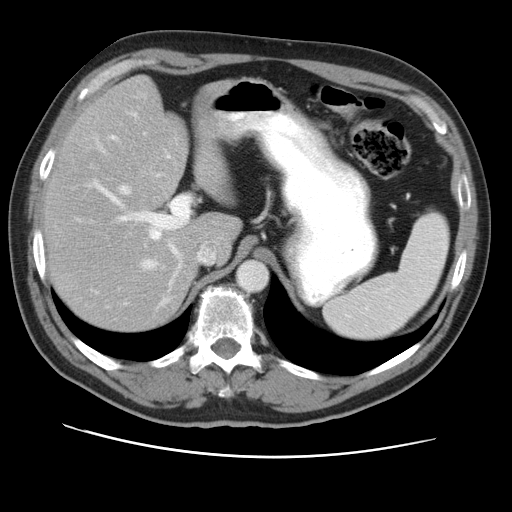
Contrast-enhanced abdominal CT, one axial slice; slice 33 of 49 in the series (ordered by position); reconstruction kernel STANDARD; intravenous contrast given; soft-tissue window (W 400 / L 40 HU); 5 mm slice thickness; 512 × 512 image matrix. Male patient, age 59 years. From the clinical record (not read from this slice): diagnosis: colorectal cancer liver metastases, imaged before liver resection; multiple liver metastases: yes; largest metastasis: 6.3 cm; disease in both lobes: yes.
Annotated regions visible in this slice (expert manual segmentation):
- hepatic veins: bounding box (x1, y1, x2, y2) in pixels: (121, 186, 215, 269)
- liver: (45, 77, 238, 332)
- planned liver remnant (the part of the liver to remain after resection): (45, 77, 238, 333)
- portal vein (with intrahepatic branches): (76, 136, 191, 288)